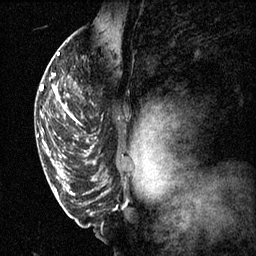
Breast MRI (dynamic contrast-enhanced), one sagittal slice; slice 44 of 60 in the series (ordered by position); 3 images stored at this slice position (order not interpretable as contrast timing); 1.5 T; TE 4.2 ms, TR 11.1 ms; 2 mm slice thickness; 256 × 256 image matrix. Female patient, age 50 years.
Outlined on this slice (semi-automatically segmented with operator editing):
- analysis volume of interest (the breast-tissue region the enhancement analysis was run in; not a lesion): bounding box <68,68,101,141> (left, top, right, bottom; pixels)
- tumour enhancement mask (voxels above the 70 % enhancement threshold inside the analysis volume of interest): <68,76,91,141>